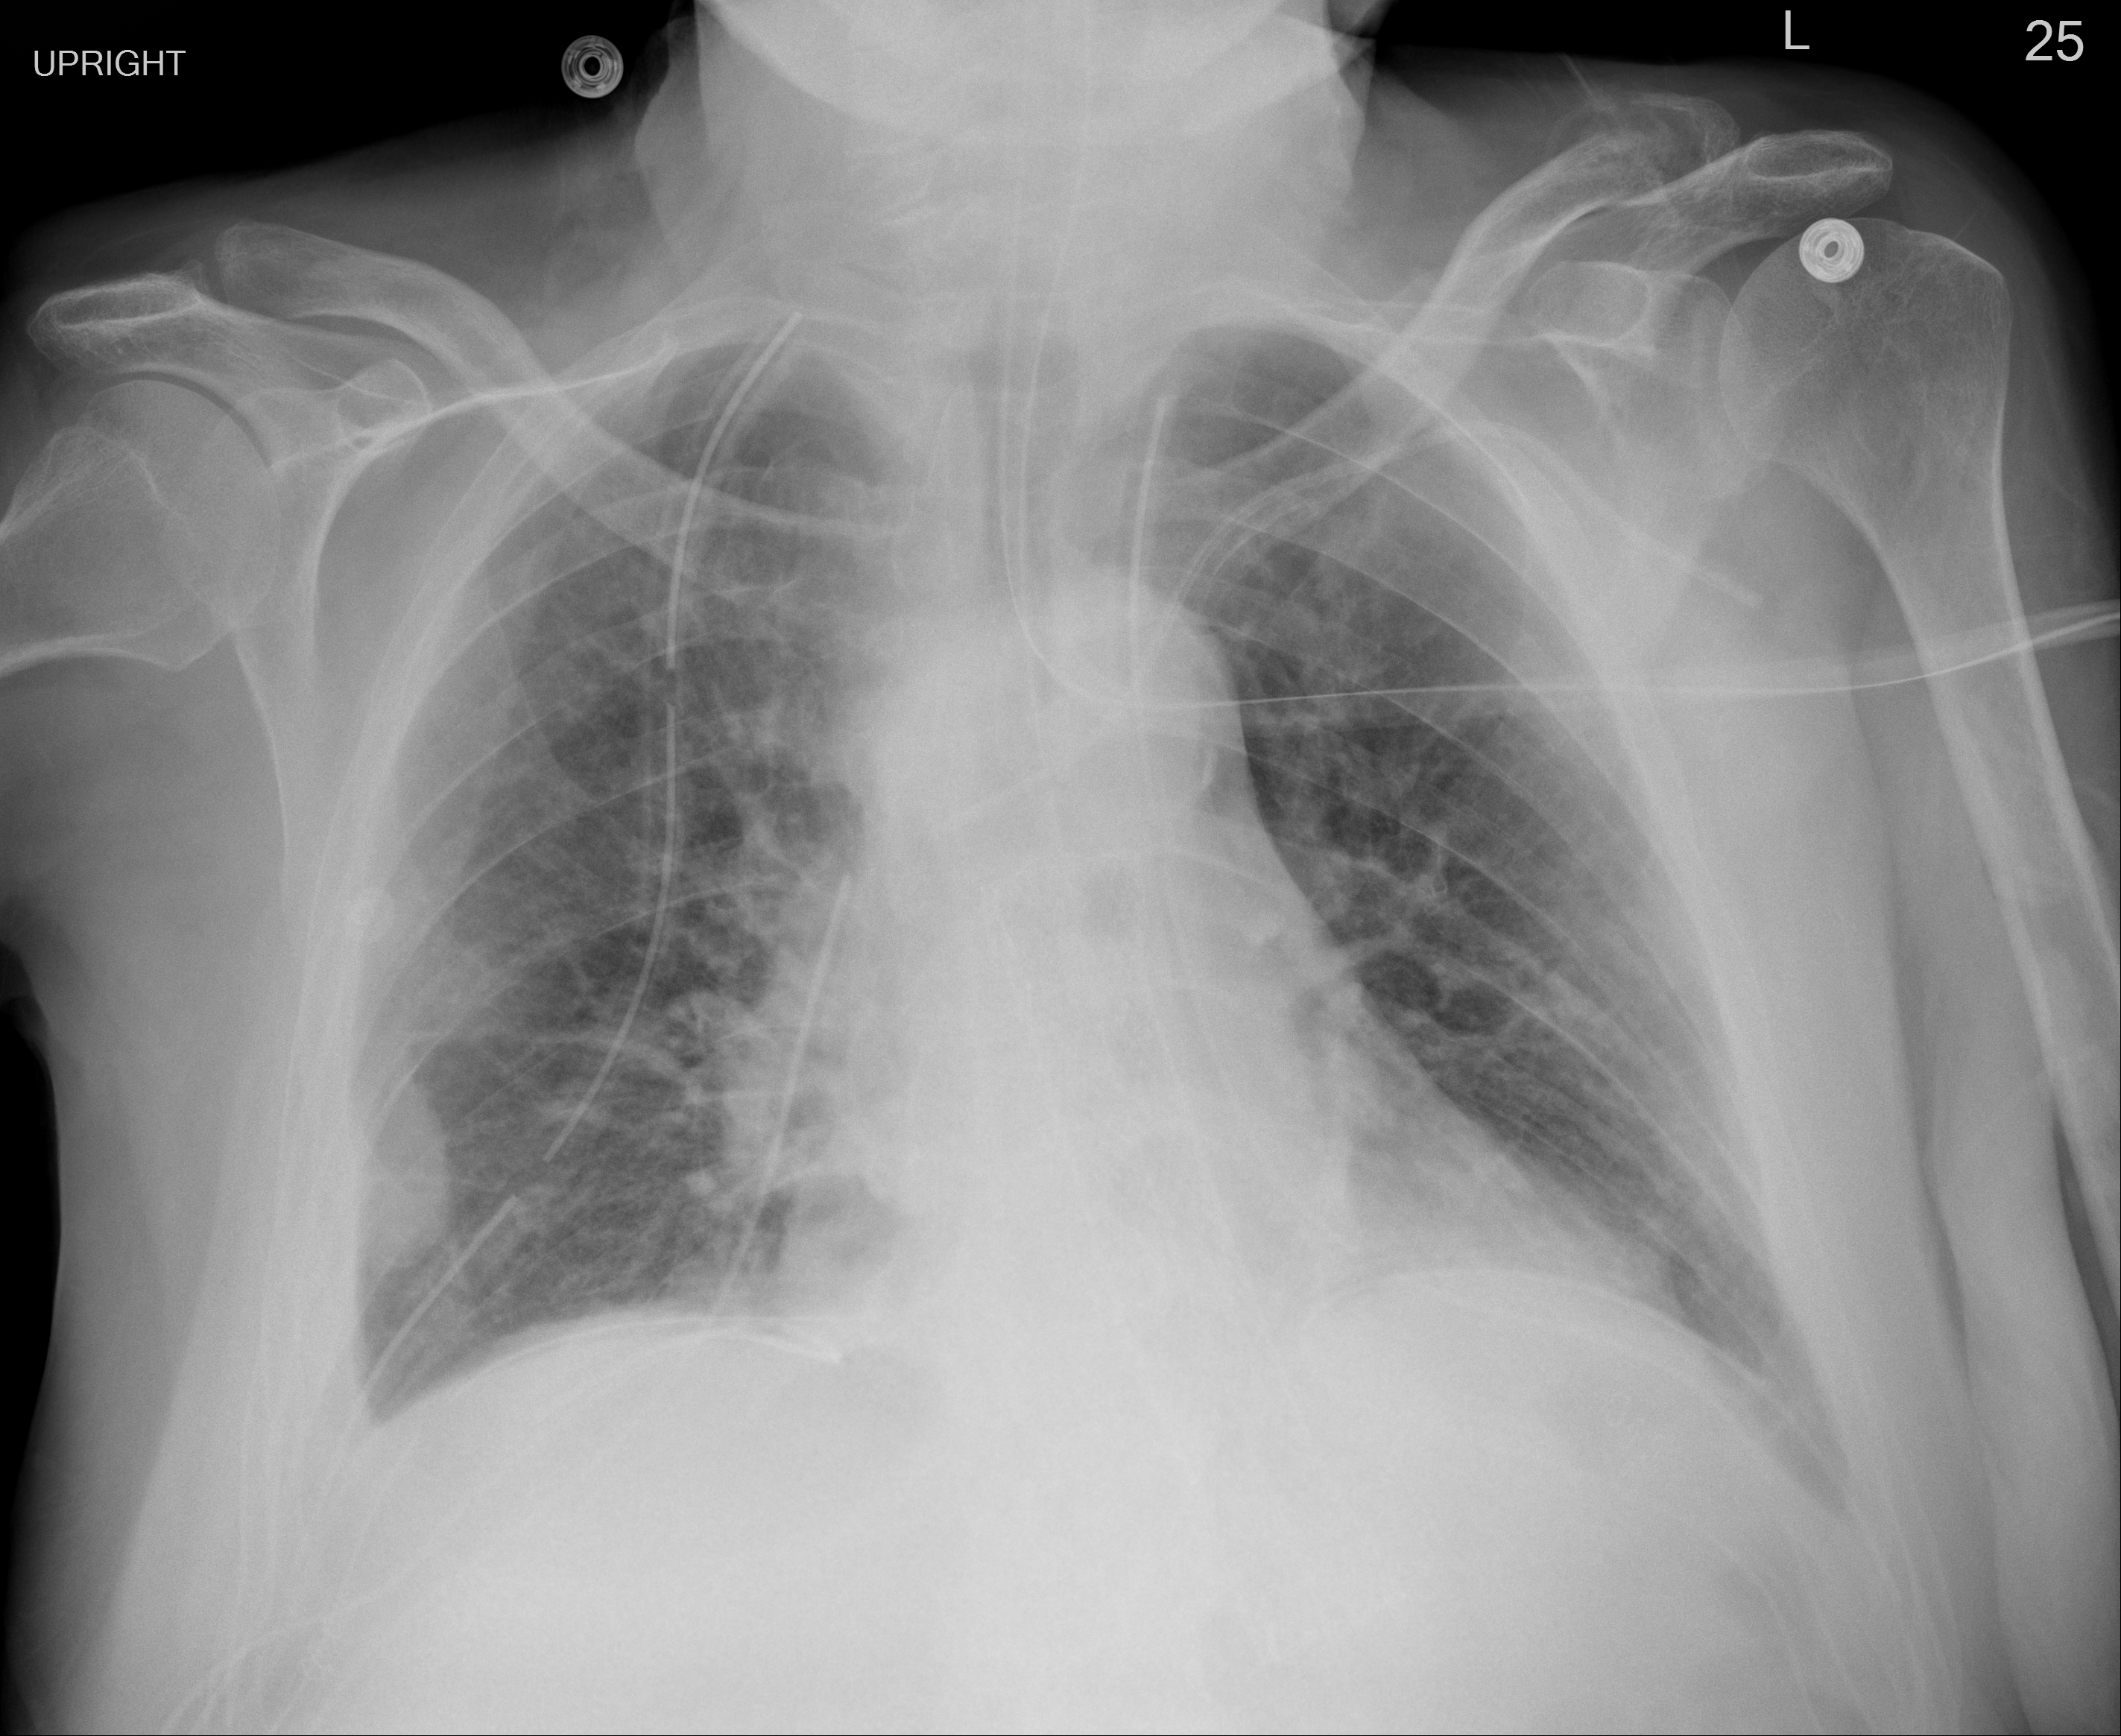
Portable chest radiograph, AP projection. Male patient, age 64 years; COVID-19 (test-positive).
Key findings recorded by the radiologist: Small right pleural effusion is seen with right lower lobe atelectasis. No pneumothorax is seen. Left basilar atelectasis is seen.